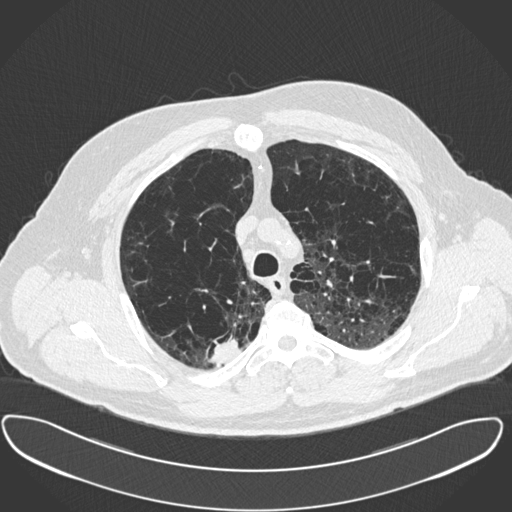
Low-dose screening chest CT, one axial slice. Slice 301 of 385 in the series (ordered by position). Reconstruction kernel B30f. Lung window (W 1500 / L -600 HU). 1 mm slice thickness. 512 × 512 image matrix, field of view 408 × 408 mm.
Structures marked on this image (manually delineated by an expert):
- lesion 1 (tumor, upper lobe of right lung): bounding box [x1, y1, x2, y2] px = [209, 339, 241, 367]